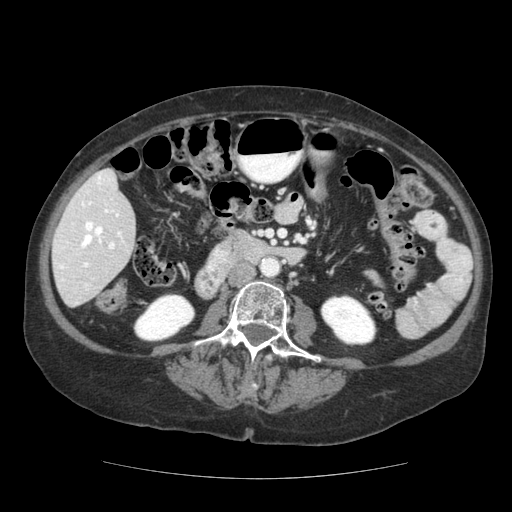
Contrast-enhanced abdominal CT (liver protocol), one axial slice. Slice 44 of 111 in the series (ordered by position). 140 kVp. Soft-tissue window (W 400 / L 40 HU). 512 × 512 image matrix. From the clinical record (not read from this slice): diagnosis: hepatocellular carcinoma (patient treated with transarterial chemoembolisation; whether this scan precedes or follows treatment is not stated here); TNM stage (as recorded): Stage-I.
Structures marked on this image (semi-automatic segmentation, software-assisted and operator-edited):
- liver parenchyma outside the tumour (the mass and vessels are separate outlines, so this box may not span the whole liver): bounding box [x1, y1, x2, y2] px = [52, 168, 136, 306]
- liver vessels: [58, 172, 124, 290]